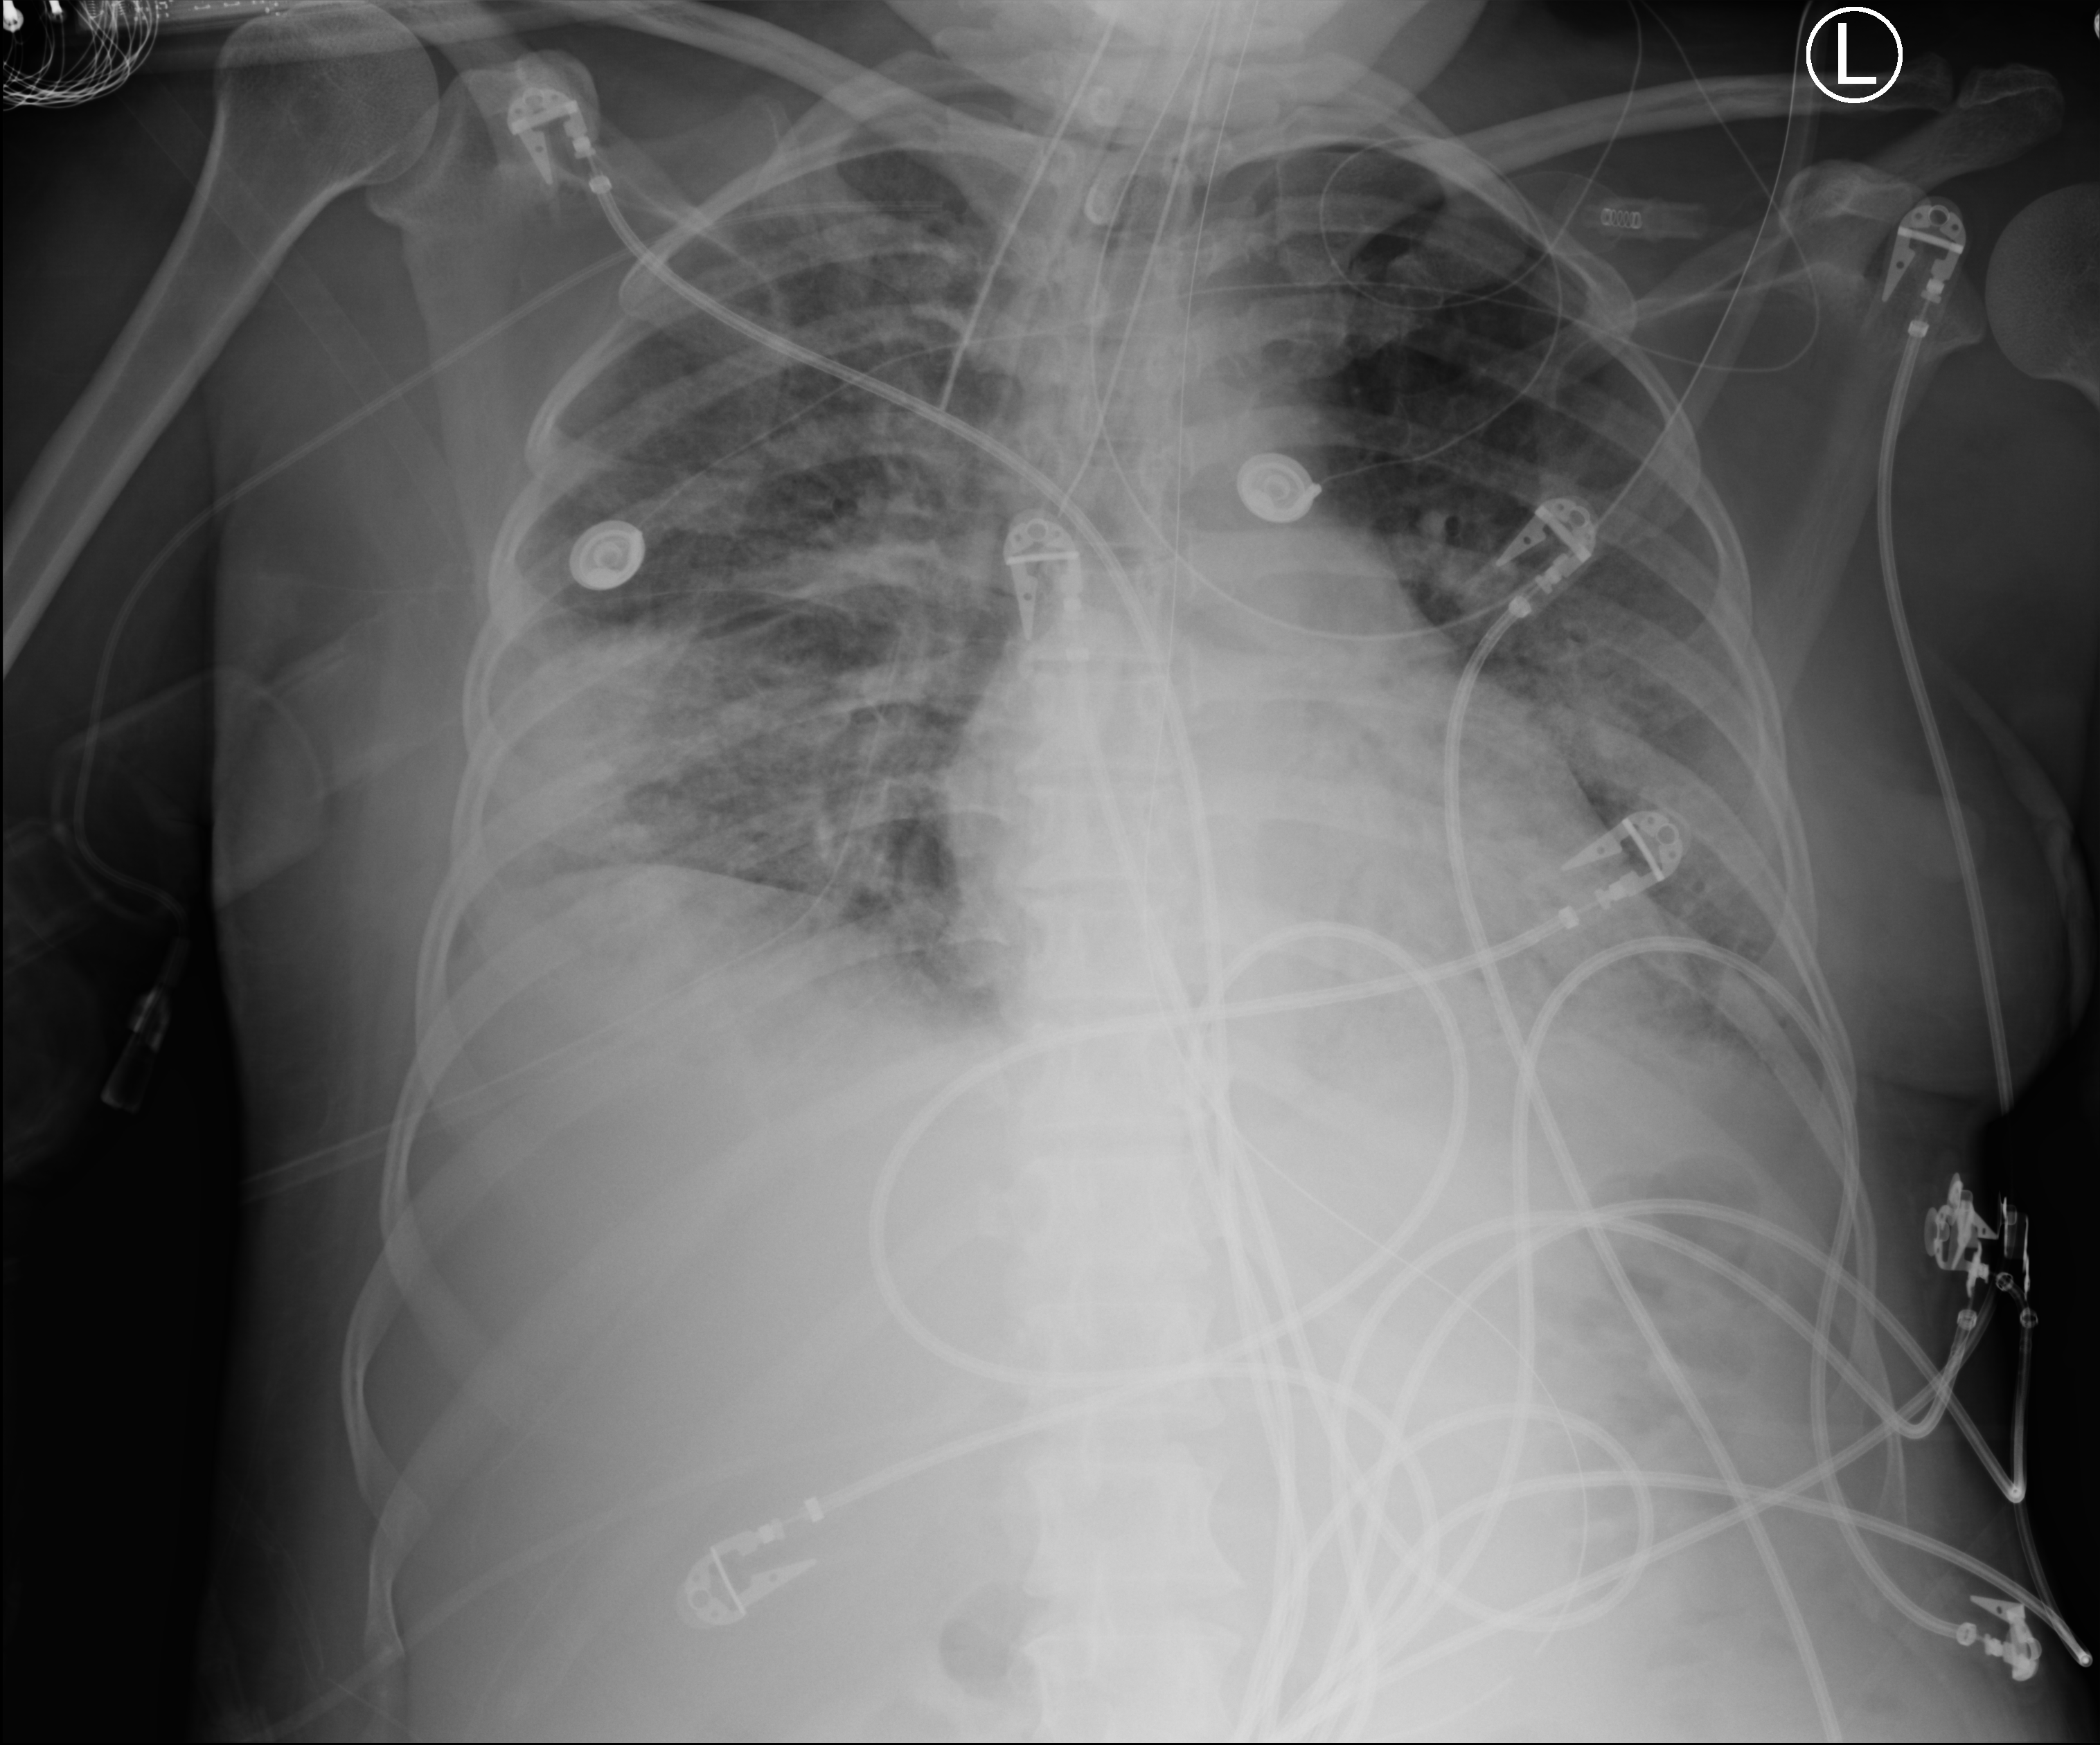
Portable chest radiograph, anteroposterior (AP) projection. Patient hospitalised with COVID-19; female, aged 18–59 years.
Hospital-stay facts (about this admission, not read from this image; timing relative to this image not recorded):
- admitted to intensive care during this hospital stay: yes
- mechanically ventilated during this hospital stay: yes
- smoking status (admission record): former